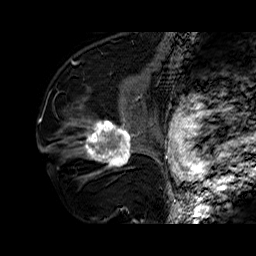
Breast MRI (dynamic contrast-enhanced), one sagittal slice. Position 37 of 60 along the scan axis. Dynamic contrast-enhanced series, time point 2 of 6 at this slice position (early post-contrast). 1.5 T. TE 6.4 ms, TR 32.7 ms. 256 × 256 image matrix, field of view 200 × 200 mm. Female patient. From the clinical record (not read from this slice): setting: breast cancer imaged before/during neoadjuvant chemotherapy; receptor status: HR-positive, HER2-negative.
Outlined on this slice (semi-automatic segmentation, software-assisted and operator-edited):
- analysis volume of interest (the breast-tissue region the enhancement analysis was run in; not a lesion): bounding box [x1, y1, x2, y2] px = [73, 110, 141, 178]
- tumour enhancement mask (voxels above the 100 % enhancement threshold inside the analysis volume of interest): [81, 121, 133, 167]